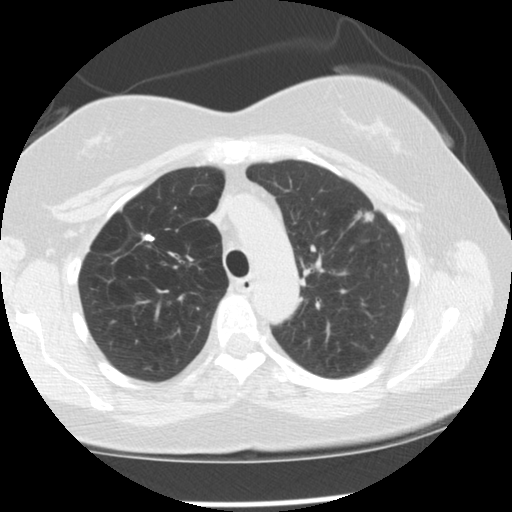
Low-dose screening chest CT, one axial slice. Slice 93 of 128 in the series (ordered by position). Reconstruction kernel STANDARD. 120 kVp. Lung window (W 1500 / L -600 HU). 2.5 mm slice thickness. 512 × 512 image matrix.
Structures marked on this image (outlined manually by an expert reader):
- lesion 1 (tumor, upper lobe of left lung): box from (x=356, y=212) to (x=374, y=222) px